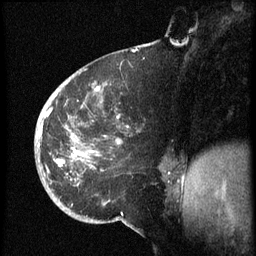
Breast MRI (dynamic contrast-enhanced), one sagittal slice. Slice 23 of 60 in the series (ordered by position). Dynamic contrast-enhanced series, image 2 of 3 at this slice position (ordered by acquisition). 1.5 T. TE 4.2 ms, TR 8.4 ms. 256 × 256 image matrix, field of view 200 × 200 mm. Female patient, age 38 years. From the clinical record (not read from this slice): setting: breast cancer imaged before/during neoadjuvant chemotherapy; receptor status: HER2-positive.
Outlined on this slice (semi-automatically segmented with operator editing):
- analysis volume of interest (the breast-tissue region the enhancement analysis was run in; not a lesion): bounding box (x1, y1, x2, y2) in pixels: (35, 74, 173, 202)
- tumour enhancement mask (voxels above the 70 % enhancement threshold inside the analysis volume of interest): (39, 88, 121, 182)